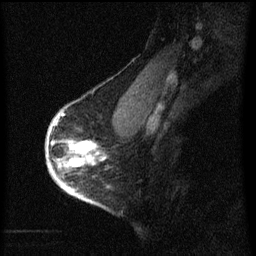
Breast MRI (dynamic contrast-enhanced), one sagittal slice. Position 45 of 60 along the scan axis. Dynamic contrast-enhanced series, image 2 of 3 at this slice position (ordered by acquisition). 1.5 T. TE 4.2 ms, TR 8 ms. 2 mm slice thickness. 256 × 256 image matrix, field of view 180 × 180 mm. Patient: female, 56 years.
Annotated regions visible in this slice (semi-automatically segmented with operator editing):
- analysis volume of interest (the breast-tissue region the enhancement analysis was run in; not a lesion): bounding box <48,110,107,193> (left, top, right, bottom; pixels)
- tumour enhancement mask (voxels above the 70 % enhancement threshold inside the analysis volume of interest): <48,114,101,193>